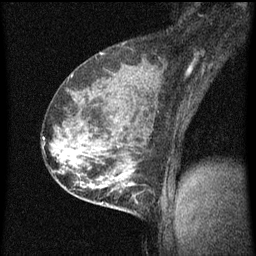
Breast MRI (dynamic contrast-enhanced), one sagittal slice. Position 39 of 60 along the scan axis. Dynamic contrast-enhanced series, image 2 of 3 at this slice position (ordered by acquisition). 1.5 T. TE 4.2 ms, TR 8 ms. 256 × 256 image matrix, field of view 180 × 180 mm. Patient: female, 35 years.
Annotated regions visible in this slice (semi-automatically segmented with operator editing):
- analysis volume of interest (the breast-tissue region the enhancement analysis was run in; not a lesion): bounding box <110,178,157,217> (left, top, right, bottom; pixels)
- tumour enhancement mask (voxels above the 70 % enhancement threshold inside the analysis volume of interest): <110,178,139,205>